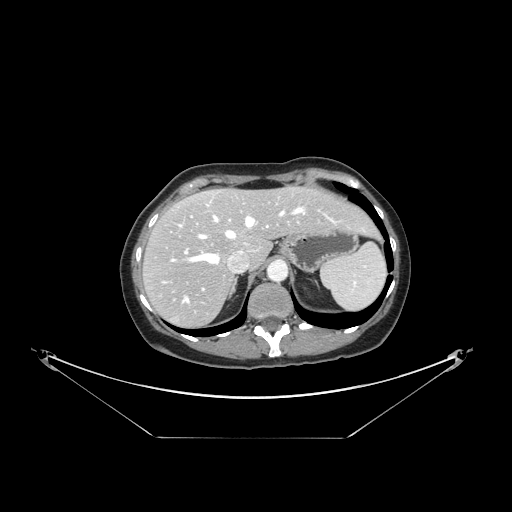
Contrast-enhanced abdominal CT, one axial slice. Slice 113 of 148 in the series (ordered by position). Reconstruction kernel STANDARD. 120 kVp. Intravenous contrast given. Soft-tissue window (W 400 / L 40 HU). 512 × 512 image matrix. Female patient, age 73 years. From the clinical record (not read from this slice): diagnosis: colorectal cancer liver metastases, imaged before liver resection; multiple liver metastases: no; largest metastasis: 1 cm; disease in both lobes: no.
Structures marked on this image (outlined manually by an expert reader):
- hepatic veins: box from (x=179, y=203) to (x=306, y=303) px
- liver: (x=144, y=188)–(x=375, y=326)
- planned liver remnant (the part of the liver to remain after resection): (x=169, y=189)–(x=375, y=264)
- portal vein (with intrahepatic branches): (x=184, y=215)–(x=334, y=291)